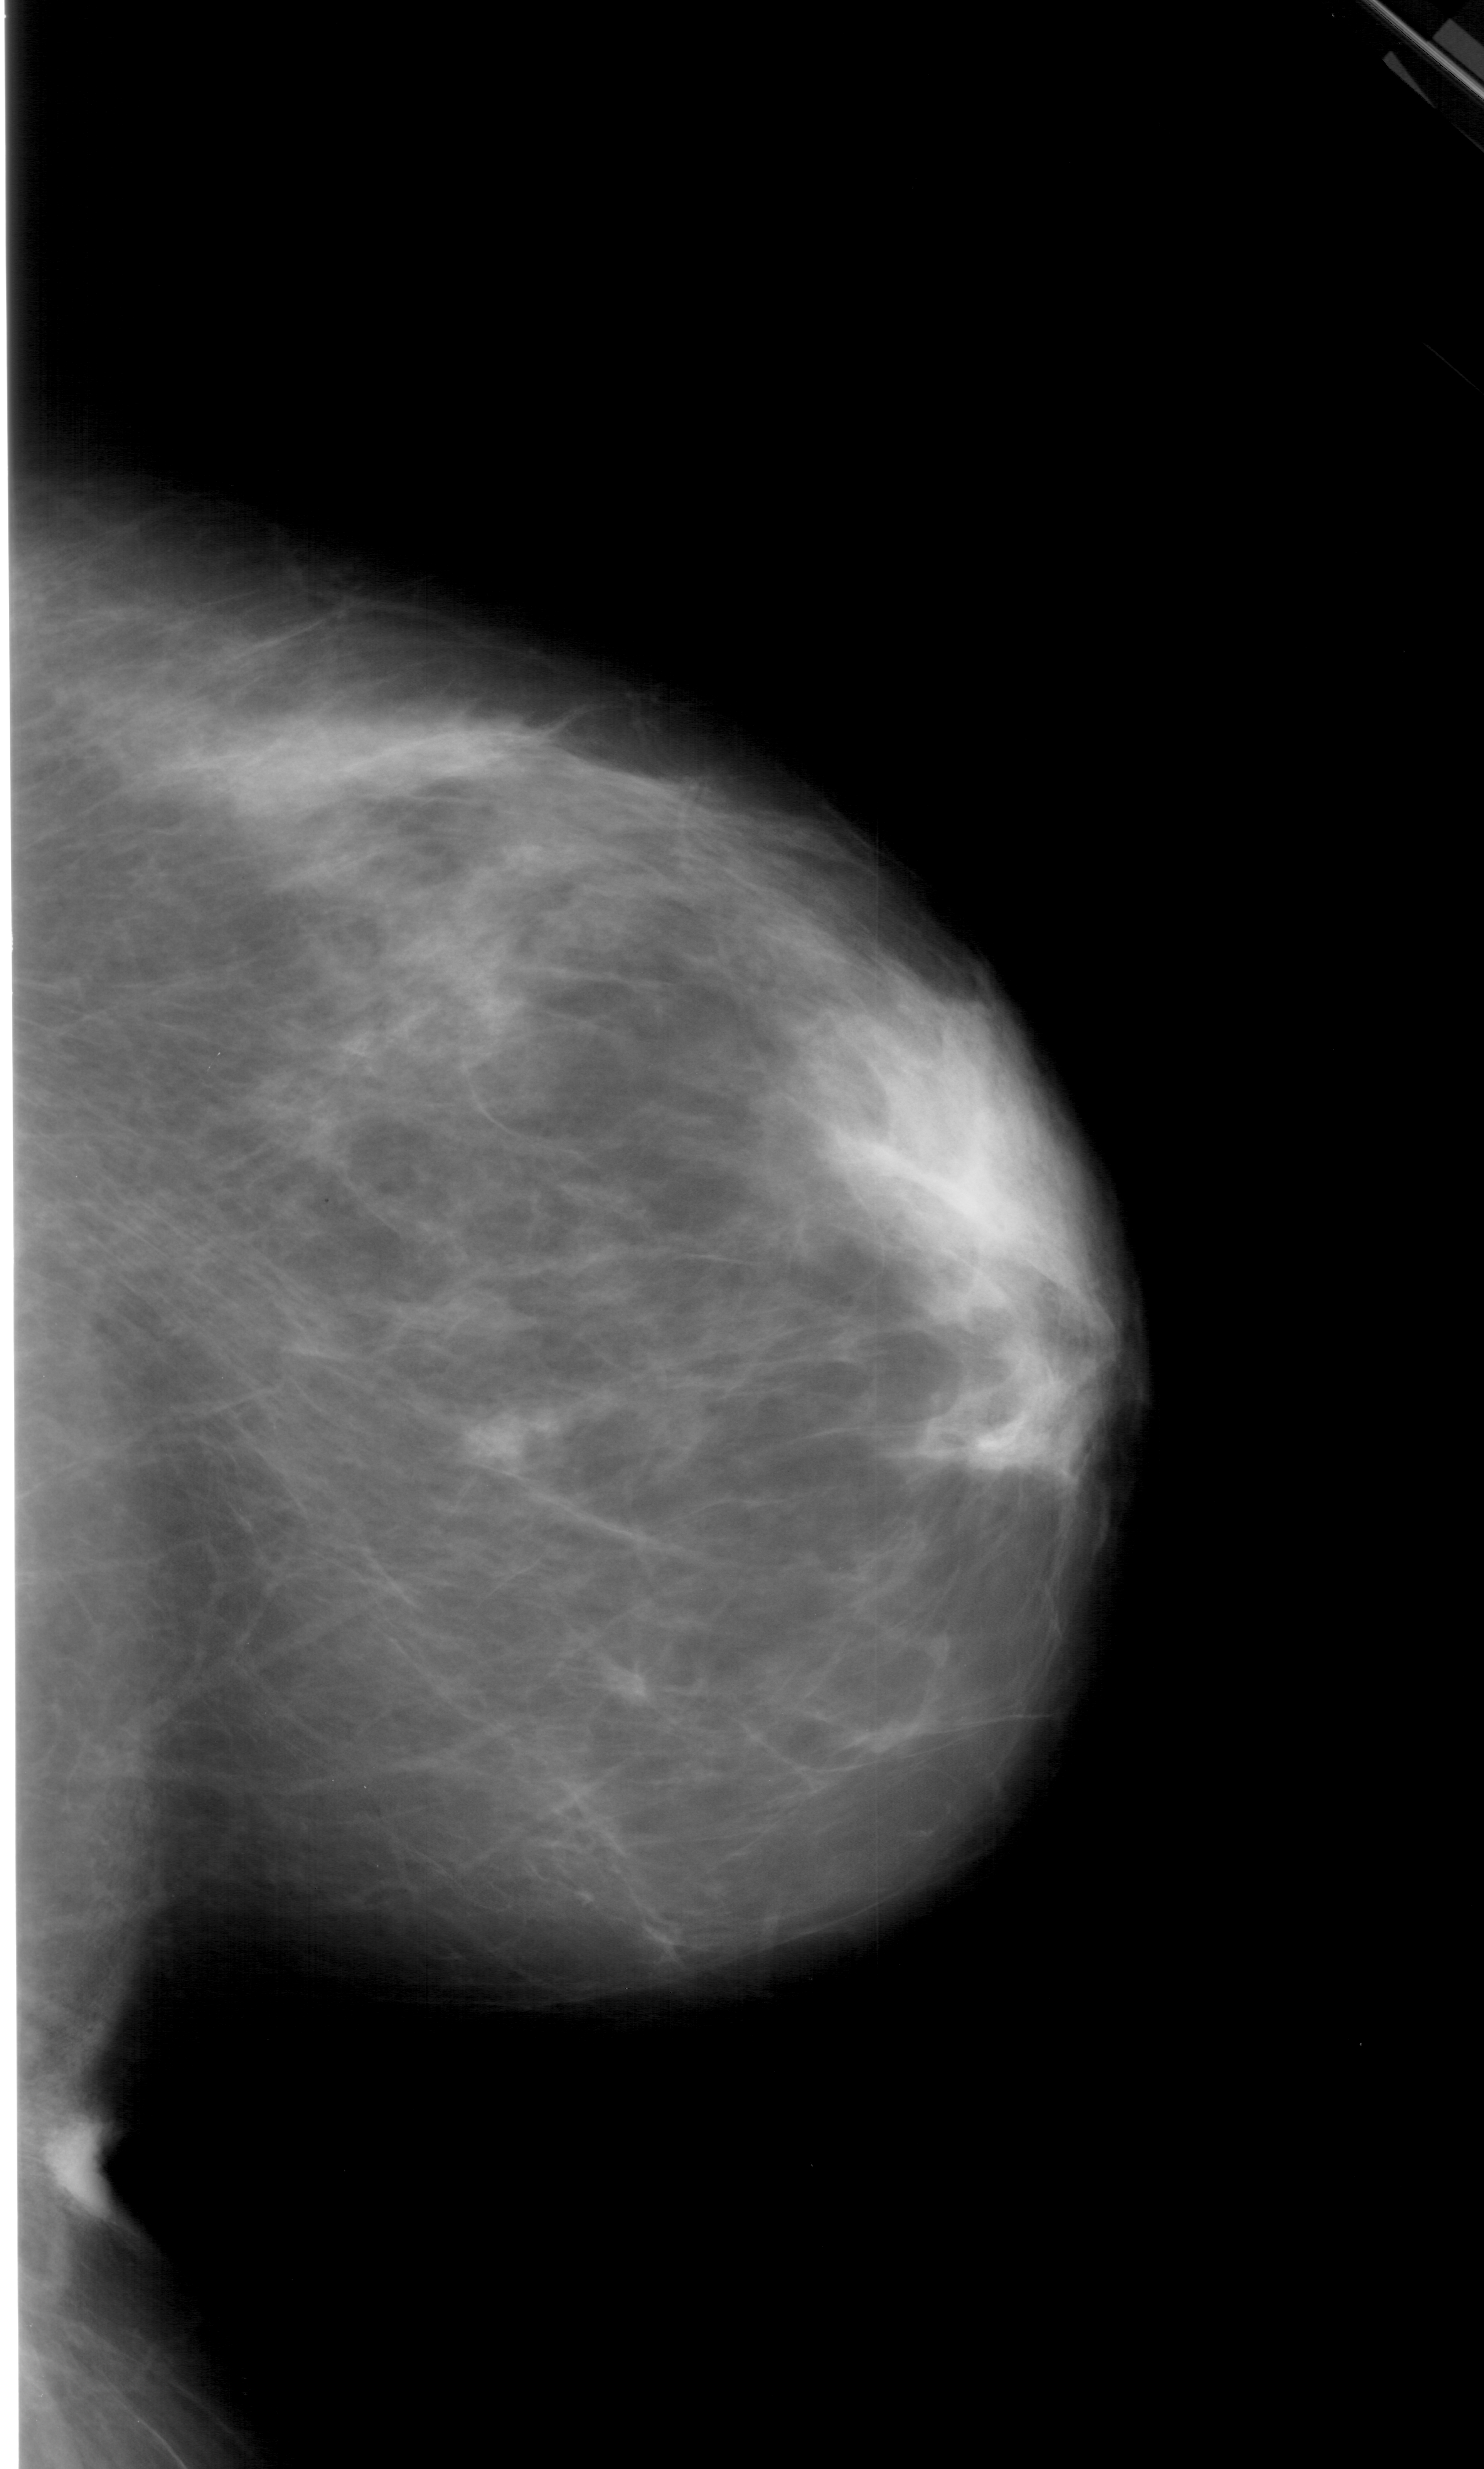
Digitized screen-film mammogram, right breast, CC view, breast composition: heterogeneously dense (BI-RADS density category 3 of 4).
Finding: mass, shape oval, margins circumscribed; BI-RADS assessment category 4; subtlety rating 3 on a 1 (subtle) to 5 (obvious) scale; pathology (as recorded): benign.